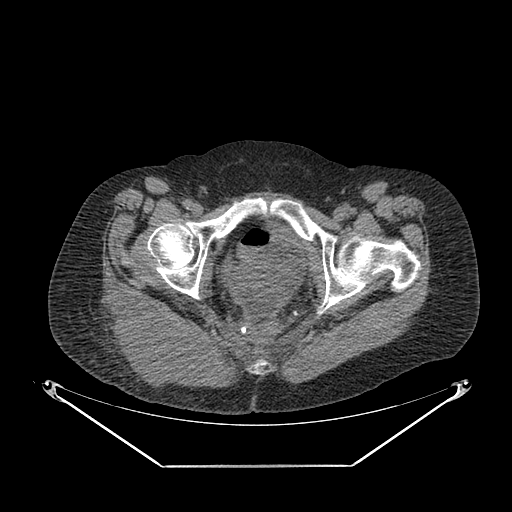
CT of an extremity soft-tissue mass (from a PET/CT study), one axial slice; reconstruction kernel SOFT; 140 kVp; soft-tissue window (W 400 / L 40 HU); 3.75 mm slice thickness; 512 × 512 image matrix, field of view 500 × 500 mm. Female patient. Case-level facts recorded for this patient, not image findings: histological type: spindle cell suggestive of myxofibrosarcoma; grade: intermediate; site of the primary tumour: right buttock.
Annotated regions visible in this slice (expert contour drawn on MRI and transferred to this co-registered scan by the dataset authors):
- gross tumour volume (mass): box from (x=105, y=299) to (x=211, y=387) px